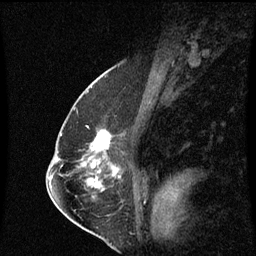
Breast MRI (dynamic contrast-enhanced), one sagittal slice. Position 37 of 60 along the scan axis. Dynamic contrast-enhanced series, image 2 of 3 at this slice position (ordered by acquisition). 1.5 T. TE 4.2 ms, TR 8.9 ms. 2 mm slice thickness. 256 × 256 image matrix. Female patient, age 57 years. From the clinical record (not read from this slice): setting: breast cancer imaged before/during neoadjuvant chemotherapy; receptor status: HR-positive, HER2-negative.
Outlined on this slice (semi-automatic segmentation, software-assisted and operator-edited):
- analysis volume of interest (the breast-tissue region the enhancement analysis was run in; not a lesion): box from (x=83, y=132) to (x=109, y=159) px
- tumour enhancement mask (voxels above the 70 % enhancement threshold inside the analysis volume of interest): (x=94, y=132)–(x=108, y=149)